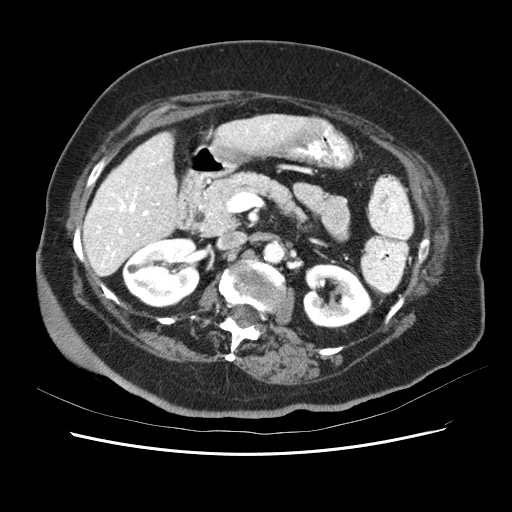
Contrast-enhanced abdominal CT (liver protocol), one axial slice. Slice 22 of 62 in the series (ordered by position). Reconstruction kernel STANDARD. 120 kVp. Soft-tissue window (W 400 / L 40 HU). 2.5 mm slice thickness. 512 × 512 image matrix, field of view 340 × 340 mm. From the clinical record (not read from this slice): diagnosis: hepatocellular carcinoma (patient treated with transarterial chemoembolisation; whether this scan precedes or follows treatment is not stated here); TNM stage (as recorded): Stage-I; Child-Pugh class: B; tumour nodularity: uninodular; tumour size: 5.3 cm.
Annotated regions visible in this slice (semi-automatically segmented with operator editing):
- liver parenchyma outside the tumour (the mass and vessels are separate outlines, so this box may not span the whole liver): bounding box <84,112,338,258> (left, top, right, bottom; pixels)
- liver vessels: <85,128,335,255>